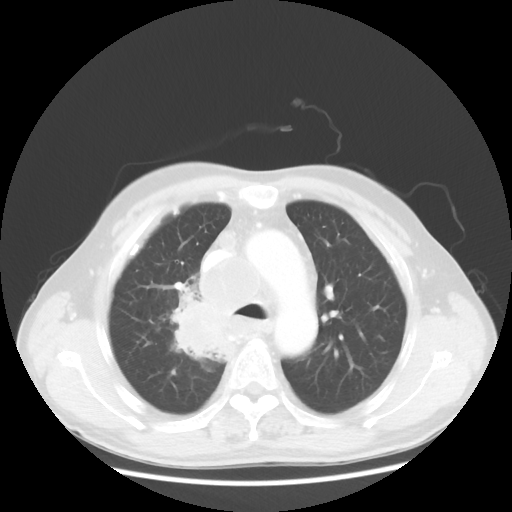
Chest CT, one axial slice. Position 87 of 124 along the scan axis. Reconstruction kernel STANDARD. Lung window (W 1500 / L -600 HU). 5 mm slice thickness. 512 × 512 image matrix. Patient: male, 64 years. From the clinical record (not read from this slice): clinical TNM (as recorded): T3 N3 M0.
Outlined on this slice (bounding box drawn by a radiologist):
- lung tumour (recorded histology: small cell carcinoma): box from (x=167, y=298) to (x=231, y=371) px